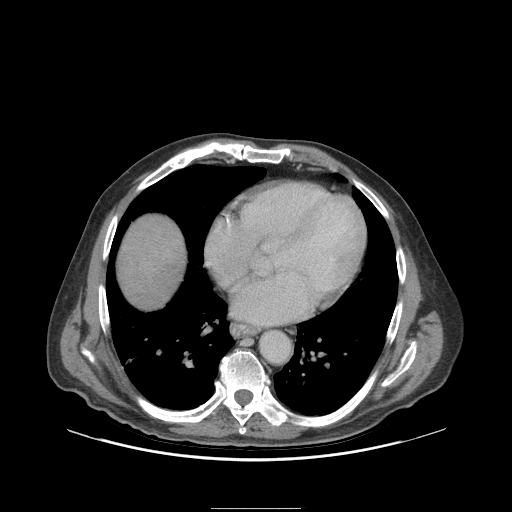
Contrast-enhanced abdominal CT (liver protocol), one axial slice. Position 97 of 105 along the scan axis. Reconstruction kernel STANDARD. Soft-tissue window (W 400 / L 40 HU). 512 × 512 image matrix, field of view 440 × 440 mm. Case-level facts recorded for this patient, not image findings: diagnosis: hepatocellular carcinoma (patient treated with transarterial chemoembolisation; whether this scan precedes or follows treatment is not stated here); TNM stage (as recorded): Stage-I; Child-Pugh class: A; tumour nodularity: uninodular.
Outlined on this slice (semi-automatic segmentation, software-assisted and operator-edited):
- liver parenchyma outside the tumour (the mass and vessels are separate outlines, so this box may not span the whole liver): box from (x=116, y=214) to (x=186, y=308) px